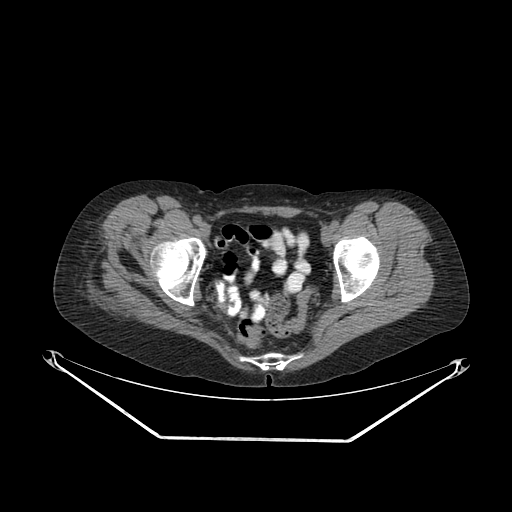
CT of an extremity soft-tissue mass (from a PET/CT study), one axial slice; position 54 of 267 along the scan axis; reconstruction kernel SOFT; soft-tissue window (W 400 / L 40 HU); 3.75 mm slice thickness; 512 × 512 image matrix, field of view 500 × 500 mm. Female patient. Case-level facts recorded for this patient, not image findings: histological type: epithelioid sarcoma with vascular differentiation; site of the primary tumour: right buttock.
Structures marked on this image (expert contour drawn on MRI and transferred to this co-registered scan by the dataset authors):
- gross tumour volume (mass): box from (x=78, y=270) to (x=134, y=321) px